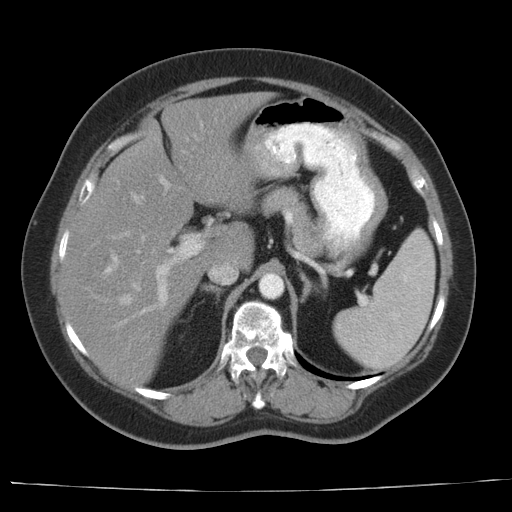
Contrast-enhanced abdominal CT, one axial slice. Slice 21 of 44 in the series (ordered by position). 140 kVp. Intravenous contrast given. Soft-tissue window (W 400 / L 40 HU). 512 × 512 image matrix, field of view 373 × 373 mm. Female patient. From the clinical record (not read from this slice): diagnosis: colorectal cancer liver metastases, imaged before liver resection; multiple liver metastases: yes; largest metastasis: 1.8 cm; disease in both lobes: no.
Outlined on this slice (outlined manually by an expert reader):
- hepatic veins: box from (x=119, y=195) to (x=143, y=304) px
- liver: (x=59, y=93)–(x=271, y=388)
- planned liver remnant (the part of the liver to remain after resection): (x=106, y=93)–(x=273, y=268)
- portal vein (with intrahepatic branches): (x=98, y=118)–(x=235, y=326)